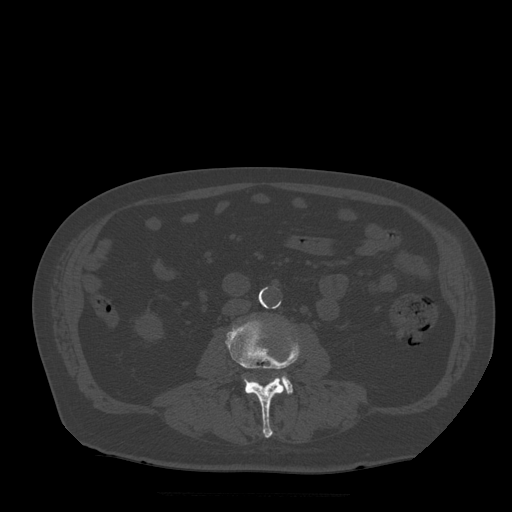
CT including the spine, one axial slice. Position 135 of 522 along the scan axis. Bone window (W 1800 / L 400 HU). 1.25 mm slice thickness. 512 × 512 image matrix, field of view 420 × 420 mm. Patient age 72 years. From the clinical record (not read from this slice): primary cancer: prostate.
Annotated regions visible in this slice (semi-automatically segmented with operator editing):
- L3 vertebra: bounding box <226,320,300,438> (left, top, right, bottom; pixels)
- L4 vertebra: <244,376,293,394>